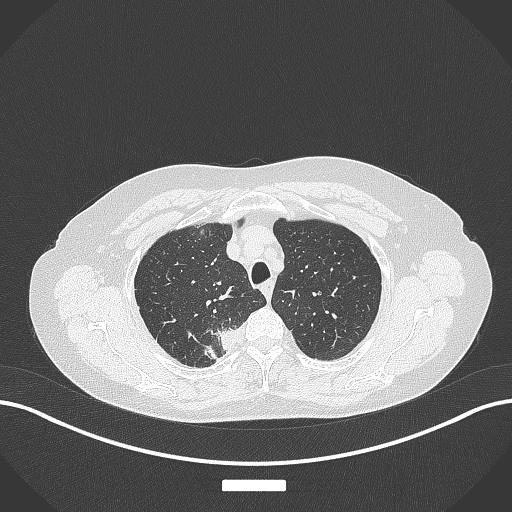
Chest CT, one axial slice. Slice 319 of 357 in the series (ordered by position). 120 kVp. Lung window (W 1500 / L -600 HU). 512 × 512 image matrix. Patient: female, 62 years. Case-level facts recorded for this patient, not image findings: clinical TNM (as recorded): T1c N1 M0.
Annotated regions visible in this slice (bounding box drawn by a radiologist):
- lung tumour (recorded histology: squamous cell carcinoma): bounding box [x1, y1, x2, y2] px = [209, 322, 246, 360]